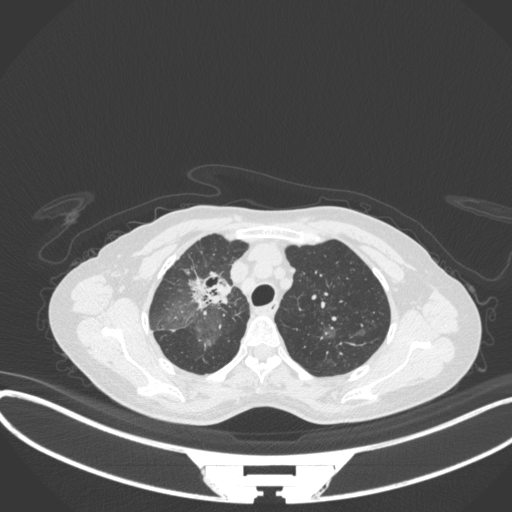
Chest CT, one axial slice; reconstruction kernel B31f; lung window (W 1500 / L -600 HU); 1 mm slice thickness; 512 × 512 image matrix, field of view 400 × 400 mm. Patient: female, 59 years. From the clinical record (not read from this slice): clinical TNM (as recorded): T3 N0 M0.
Structures marked on this image (bounding box drawn by a radiologist):
- lung tumour (recorded histology: adenocarcinoma): bounding box (x1, y1, x2, y2) in pixels: (184, 267, 237, 317)